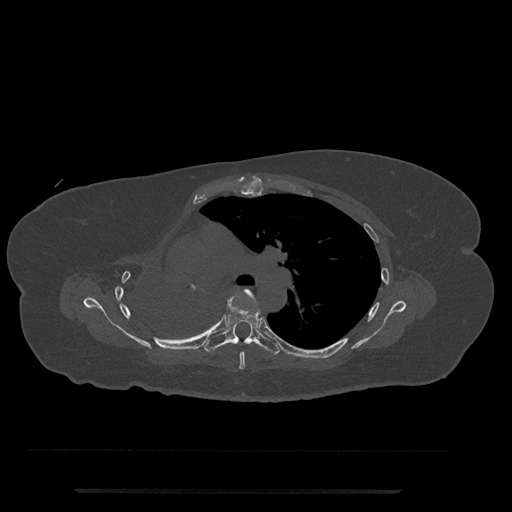
CT including the spine, one axial slice; position 511 of 797 along the scan axis; reconstruction kernel Br40s/3; 120 kVp; bone window (W 1800 / L 400 HU); 0.5 mm slice thickness; 512 × 512 image matrix, field of view 440 × 440 mm. Patient: female, 51 years. Case-level facts recorded for this patient, not image findings: primary cancer: neuro; vertebrae with lytic lesions (as recorded): T8.
Outlined on this slice (semi-automatically segmented with operator editing):
- T5 vertebra: bounding box (x1, y1, x2, y2) in pixels: (239, 289, 265, 370)
- T6 vertebra: (204, 300, 281, 355)